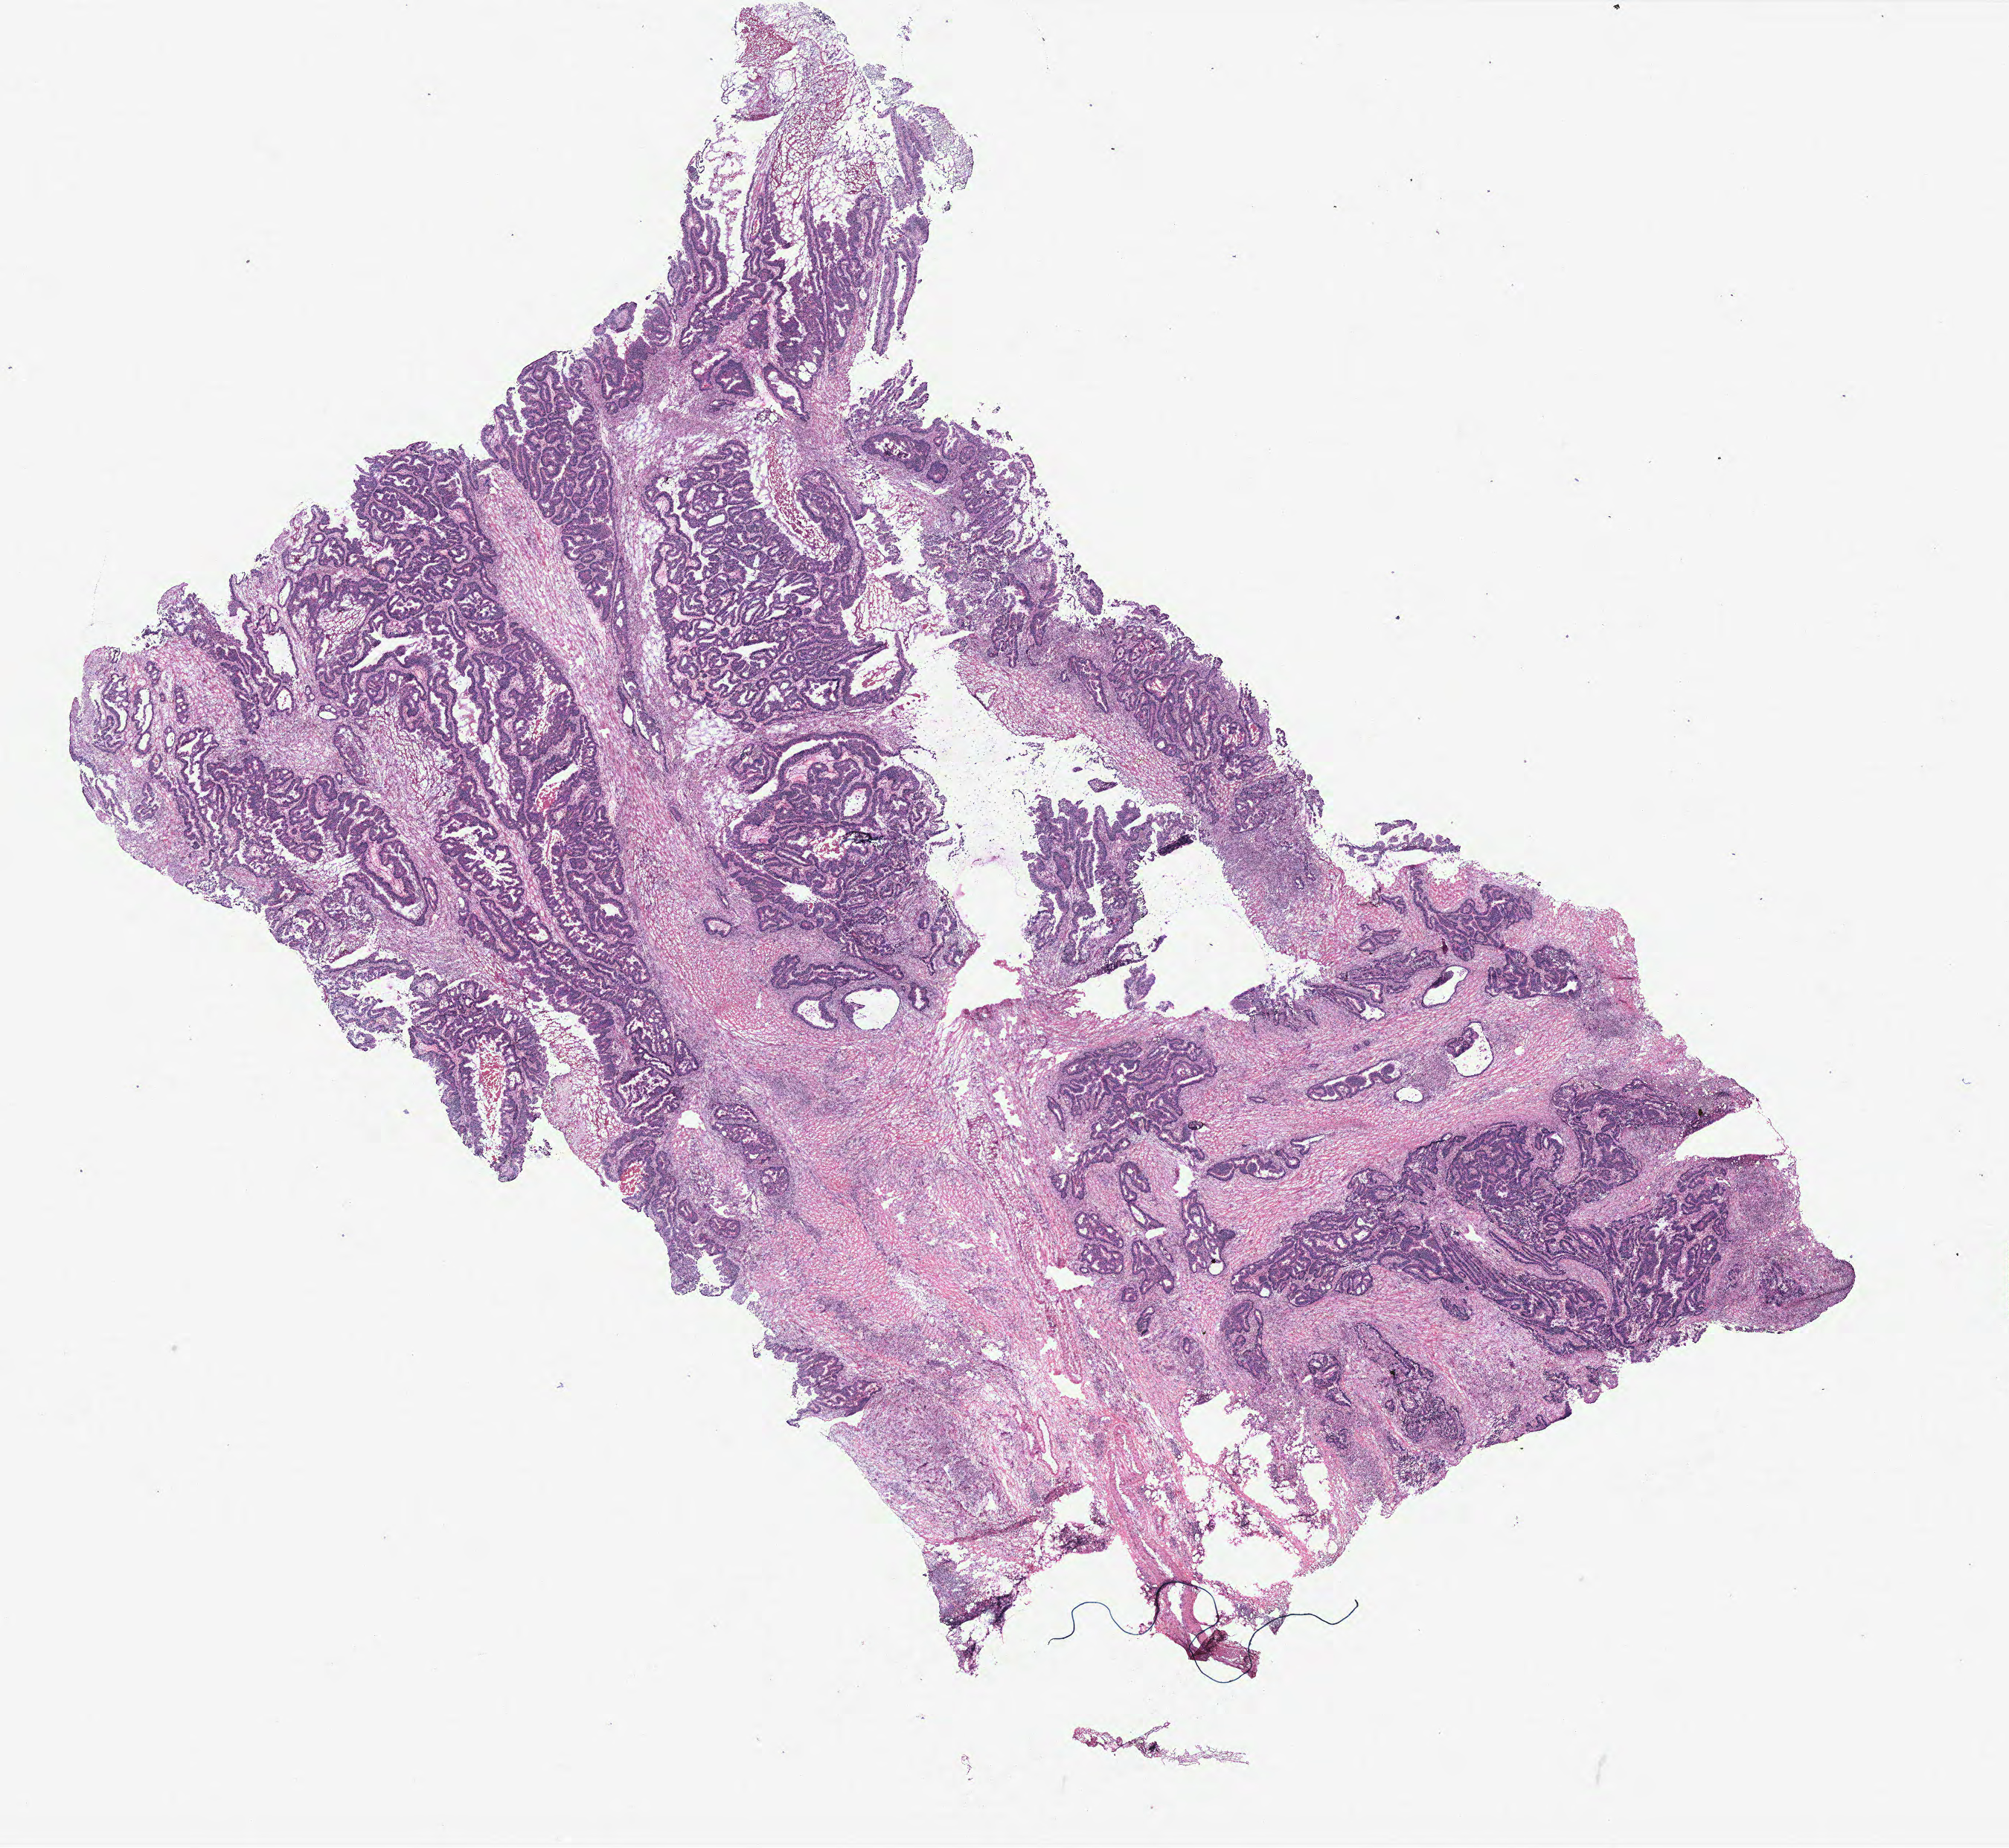
Digitized Hematoxylin and eosin (H&E) stained tissue section (whole slide) — a low-resolution overview of the entire scanned area, about 21.6 x 19.9 mm (slide scanned at 40x); colon, normal (non-tumour) tissue. Patient: female, age 71 years.
This section: normal (non-tumour) tissue from the same patient. Patient diagnosis: Adenocarcinoma, NOS.